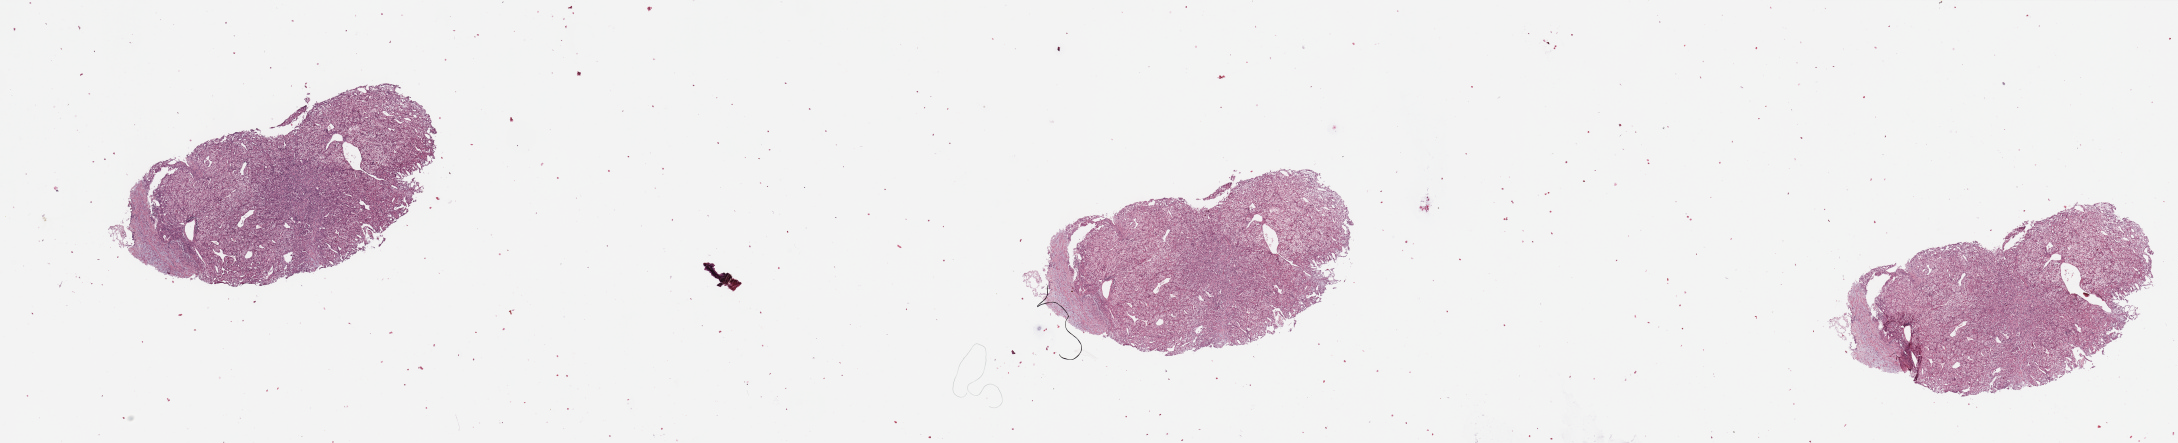
Digitized H&E tissue section (whole slide), whole scanned area (about 34.5 x 7.0 mm, slide scanned at 20x) shown as a low-resolution overview. Tumour tissue sample, sampled site: kidney. 58-year-old male patient. Histologic grade: G3 (poorly differentiated). Slide review estimates, as recorded: tumour nuclei 90%, necrosis 0%.
- histologic diagnosis: Renal cell carcinoma, NOS
- AJCC pathologic stage: II